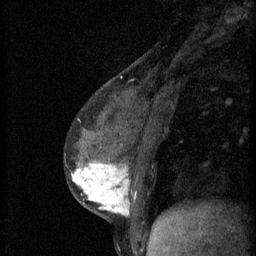
Breast MRI (dynamic contrast-enhanced), one sagittal slice; slice 23 of 60 in the series (ordered by position); 3 images stored at this slice position (order not interpretable as contrast timing); 1.5 T; TE 4.2 ms, TR 11 ms; 2 mm slice thickness; 256 × 256 image matrix, field of view 180 × 180 mm. Patient: female, 37 years.
Annotated regions visible in this slice (semi-automatic segmentation, software-assisted and operator-edited):
- analysis volume of interest (the breast-tissue region the enhancement analysis was run in; not a lesion): box from (x=65, y=138) to (x=174, y=221) px
- tumour enhancement mask (voxels above the 70 % enhancement threshold inside the analysis volume of interest): (x=72, y=162)–(x=129, y=217)